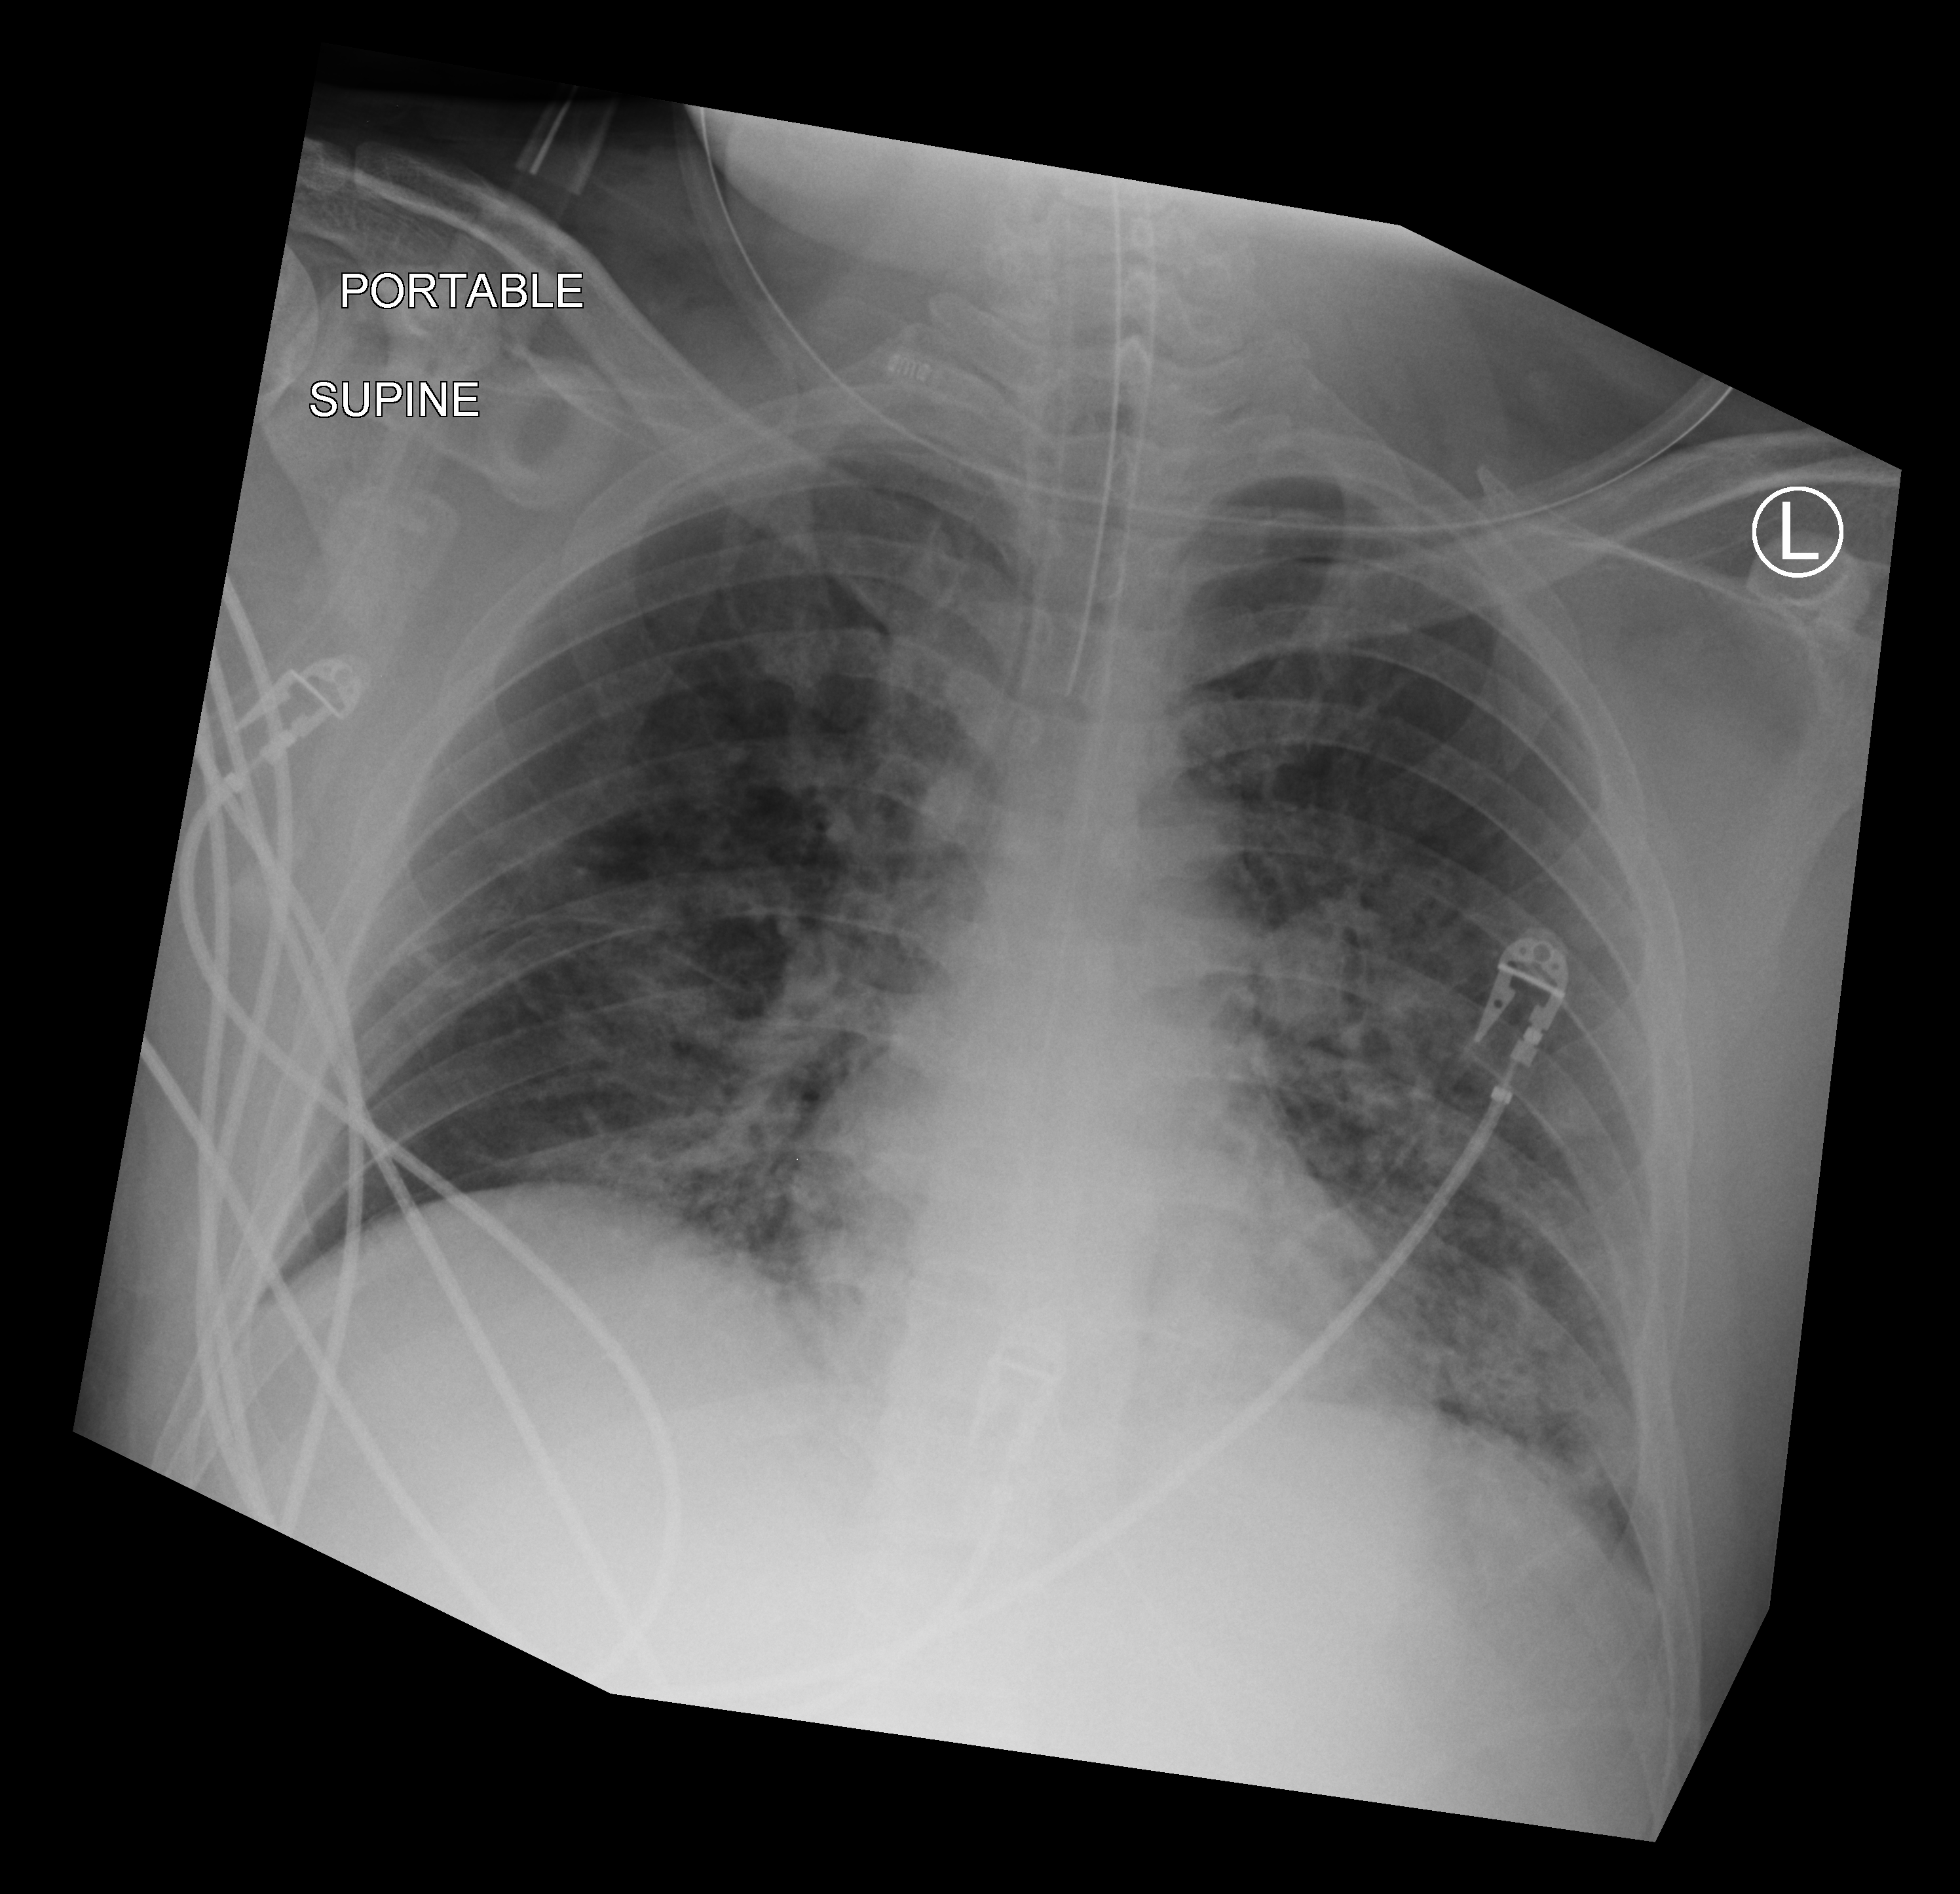
Chest X-ray (portable), anteroposterior (AP) projection. Patient hospitalised with COVID-19, aged 18–59 years.
From the hospital-stay record, not from the radiograph (when in the stay this image was taken is not recorded):
- length of hospital stay: 60 days